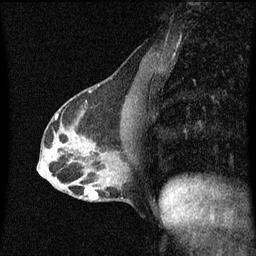
Breast MRI (dynamic contrast-enhanced), one sagittal slice. Slice 26 of 60 in the series (ordered by position). Dynamic contrast-enhanced series, image 2 of 3 at this slice position (ordered by acquisition). 1.5 T. TE 4.2 ms, TR 8.4 ms. 256 × 256 image matrix. Female patient, age 40 years.
Outlined on this slice (semi-automatically segmented with operator editing):
- analysis volume of interest (the breast-tissue region the enhancement analysis was run in; not a lesion): box from (x=78, y=166) to (x=120, y=203) px
- tumour enhancement mask (voxels above the 70 % enhancement threshold inside the analysis volume of interest): (x=81, y=188)–(x=99, y=201)